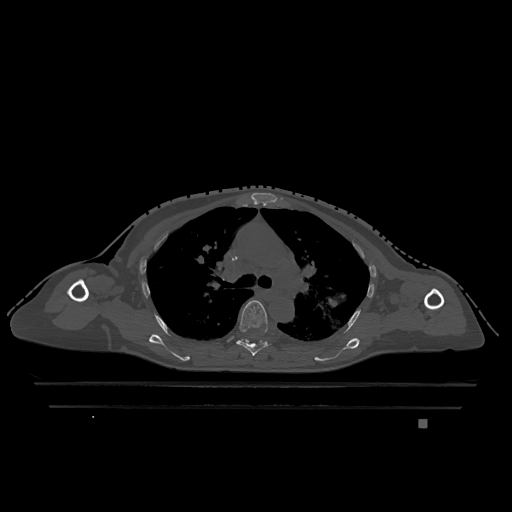
CT including the spine, one axial slice; slice 831 of 1317 in the series (ordered by position); bone window (W 1800 / L 400 HU); 0.5 mm slice thickness; 512 × 512 image matrix. Patient: female, 74 years. Case-level facts recorded for this patient, not image findings: primary cancer: lung.
Outlined on this slice (semi-automatic segmentation, software-assisted and operator-edited):
- T5 vertebra: bounding box (x1, y1, x2, y2) in pixels: (236, 300, 270, 356)
- T6 vertebra: (240, 339, 243, 342)